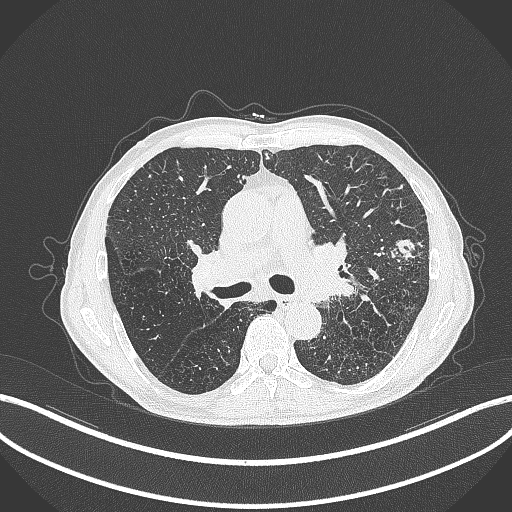
Chest CT, one axial slice; slice 257 of 463 in the series (ordered by position); reconstruction kernel B70f; lung window (W 1500 / L -600 HU); 1 mm slice thickness; 512 × 512 image matrix, field of view 400 × 400 mm. Patient: male, 74 years. From the clinical record (not read from this slice): clinical TNM (as recorded): T2a N1 M0.
Annotated regions visible in this slice (rectangle marked by the reading radiologist):
- lung tumour (recorded histology: adenocarcinoma): box from (x=382, y=234) to (x=418, y=261) px